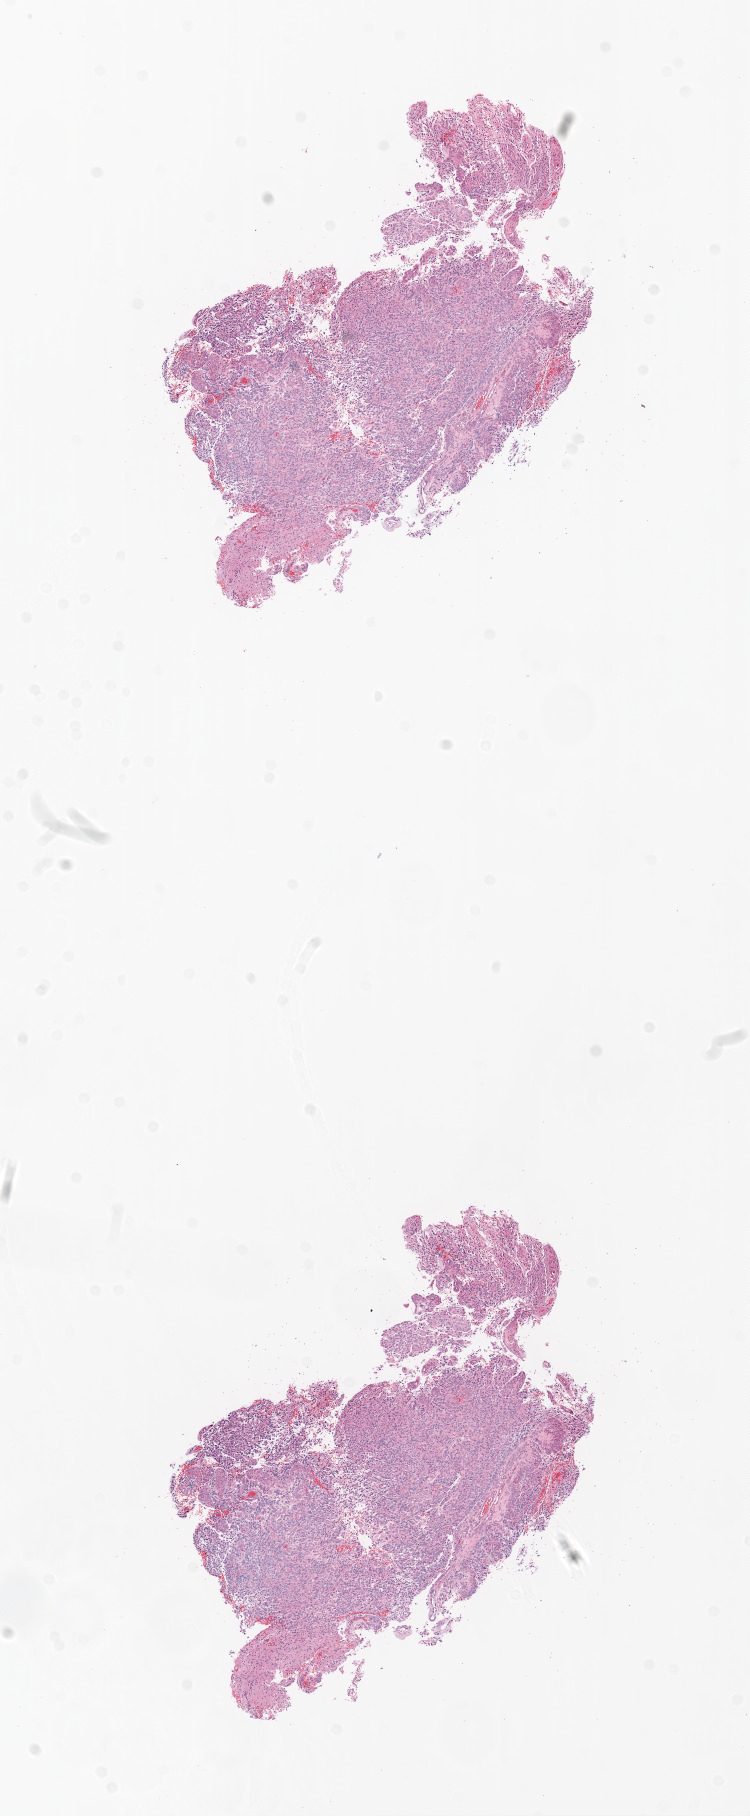
Whole-slide histology image, H&E — low-resolution overview of the scanned area, about 6.0 x 14.6 mm (slide scanned at 20x); formalin-fixed paraffin-embedded (FFPE) diagnostic section; brain, primary tumour sample. Male patient; age at initial diagnosis 53 years.
* pathologic diagnosis: Glioblastoma